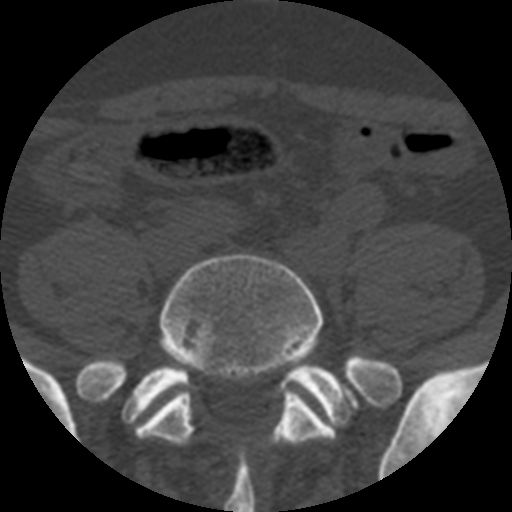
CT including the spine, one axial slice; slice 56 of 508 in the series (ordered by position); bone window (W 1800 / L 400 HU); 1.25 mm slice thickness; 512 × 512 image matrix. Patient age 57 years. Case-level facts recorded for this patient, not image findings: primary cancer: prostate.
Outlined on this slice (semi-automatic segmentation, software-assisted and operator-edited):
- L5 vertebra: bounding box <135,254,391,446> (left, top, right, bottom; pixels)